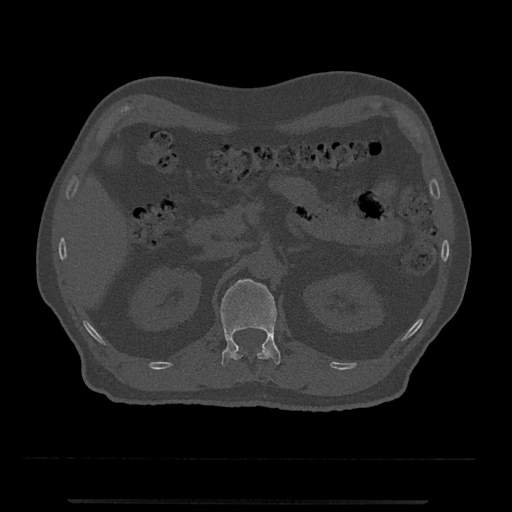
CT including the spine, one axial slice. Position 357 of 797 along the scan axis. 120 kVp. Bone window (W 1800 / L 400 HU). 0.5 mm slice thickness. 512 × 512 image matrix, field of view 419 × 419 mm. Patient: male, 63 years. From the clinical record (not read from this slice): primary cancer: prostate.
Annotated regions visible in this slice (semi-automatically segmented with operator editing):
- L1 vertebra: box from (x=220, y=278) to (x=281, y=367) px
- T12 vertebra: (x=231, y=346)–(x=271, y=360)